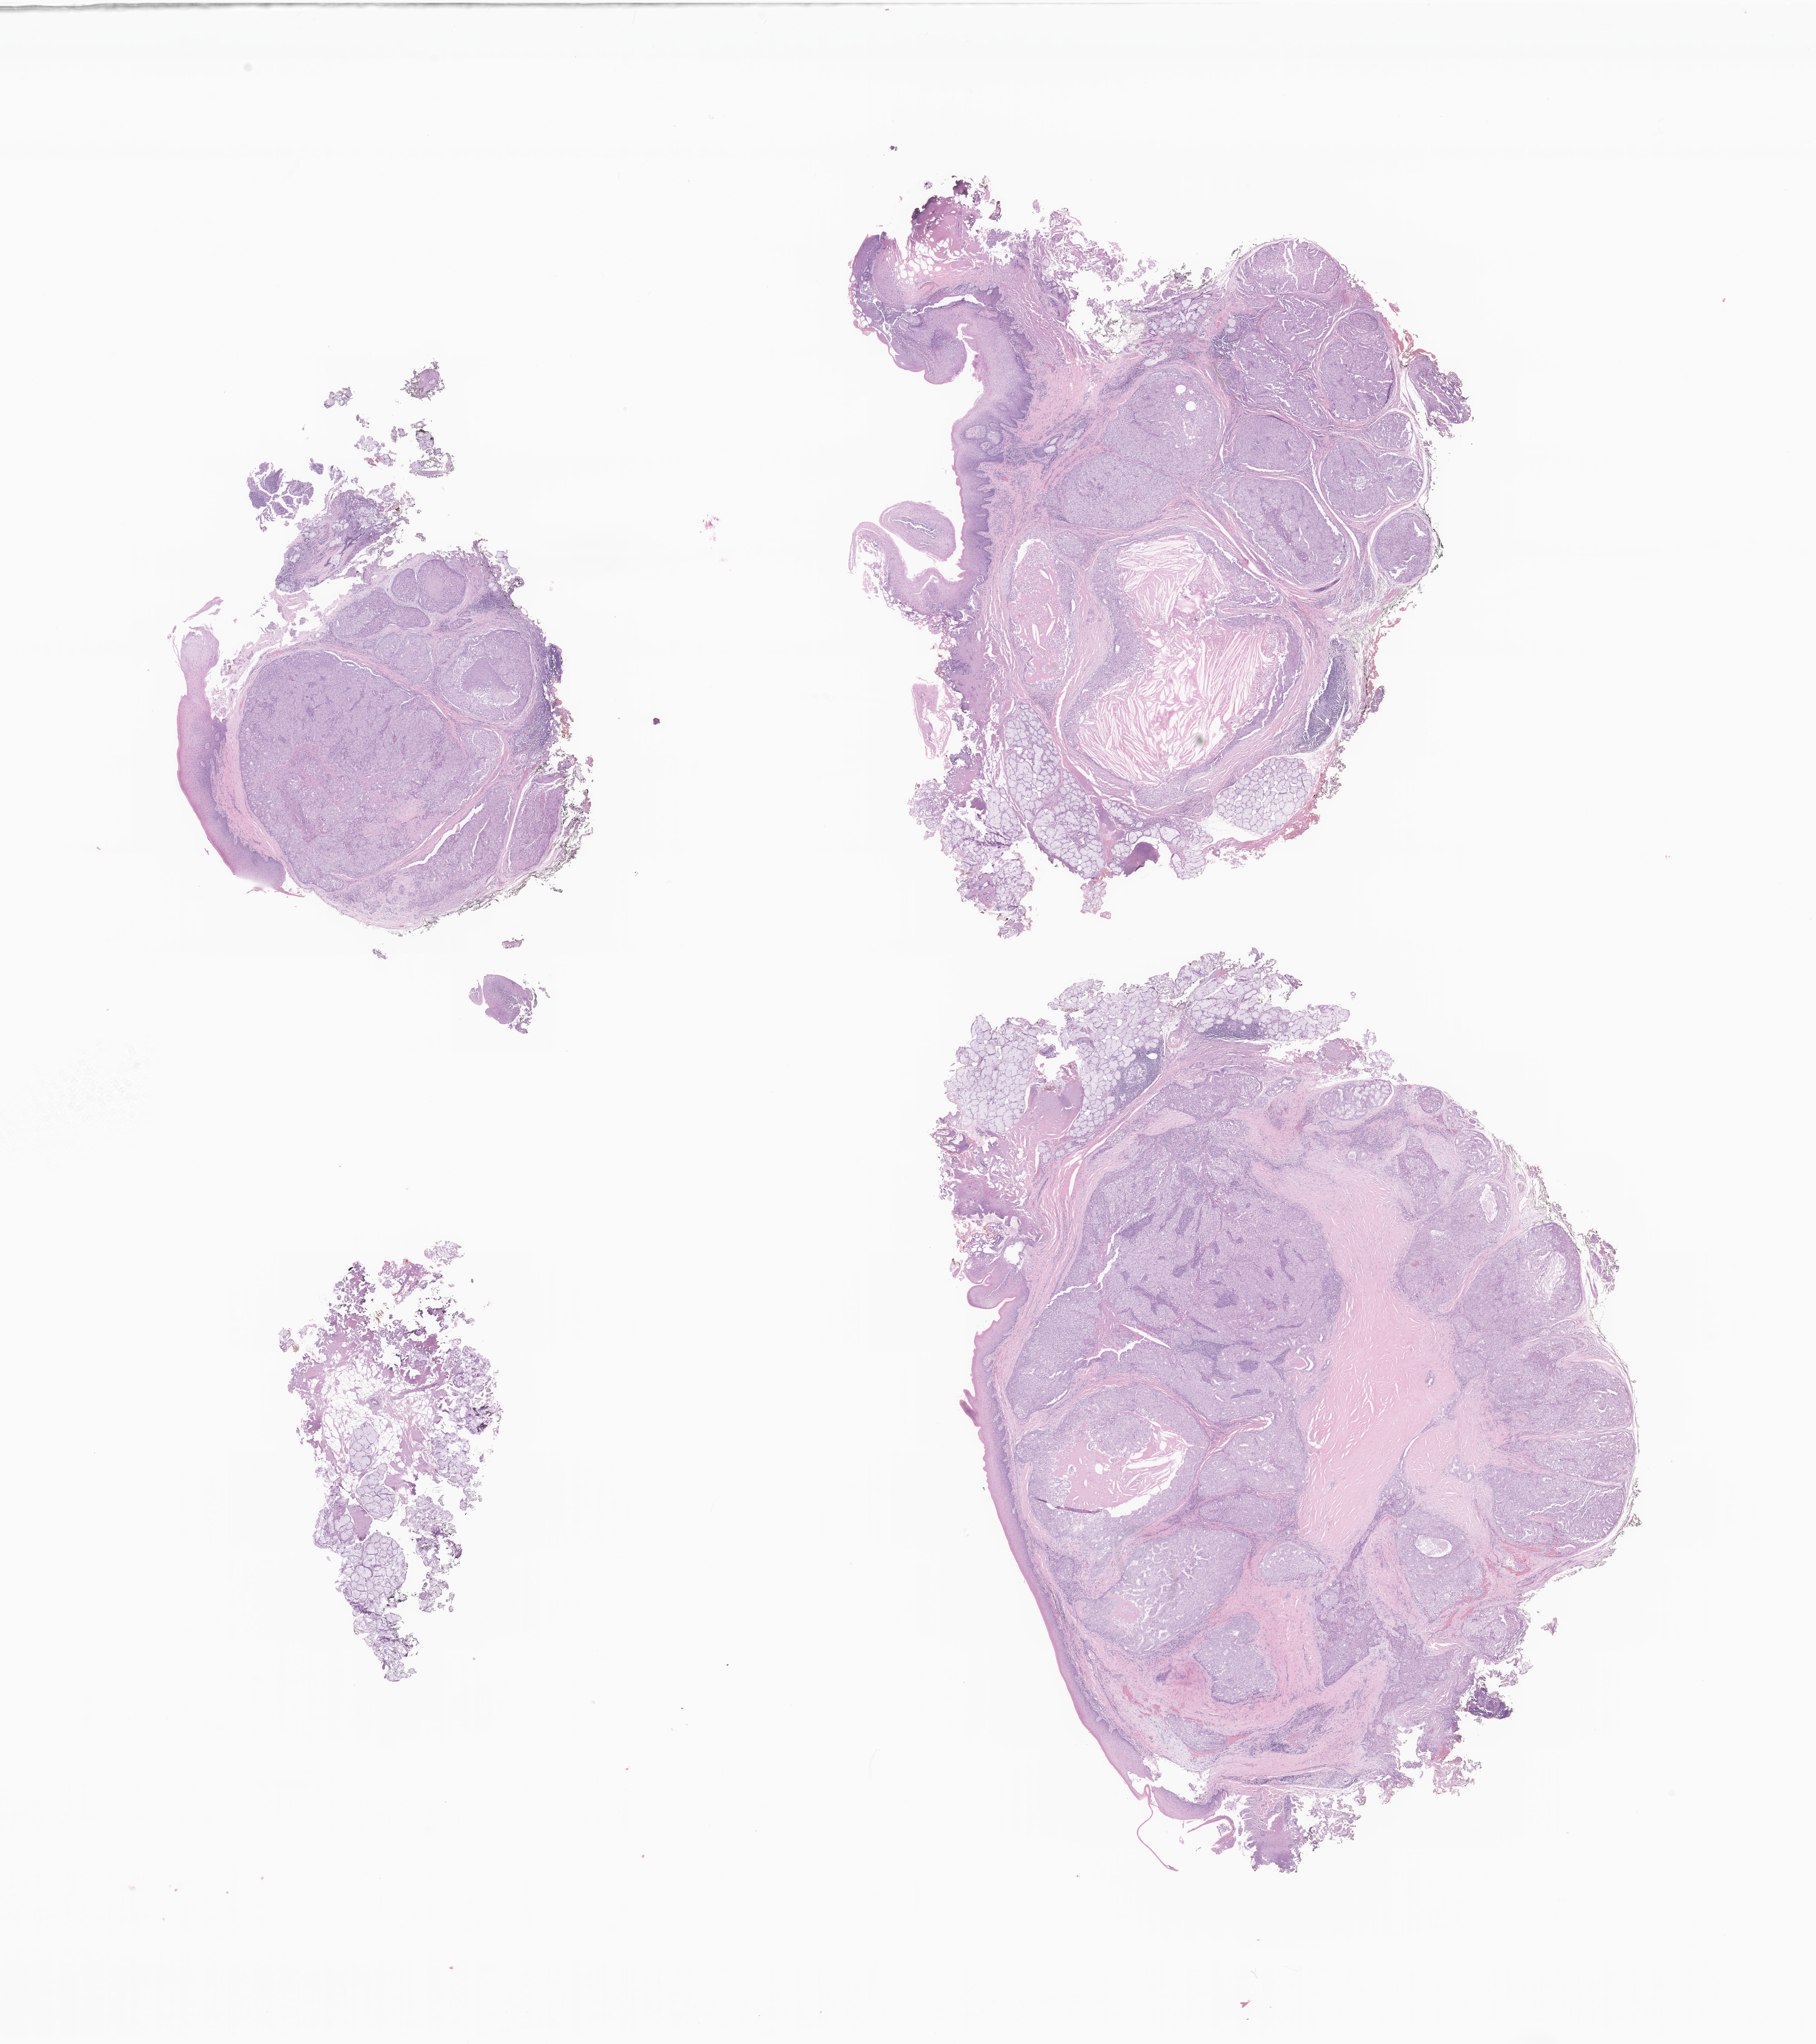
Digitized H&E-stained section of tumor tissue from the mouth and/or pharynx — a low-resolution overview of the entire scanned area, about 19.5 x 22.0 mm; FFPE section. Patient male; age 199 months (16 years 7 months).
- diagnosis: Epithelial-myoepithelial carcinoma